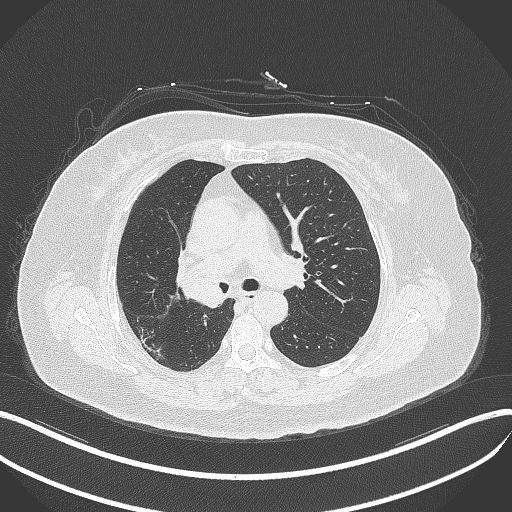
Chest CT, one axial slice; position 225 of 376 along the scan axis; reconstruction kernel B70f; 120 kVp; lung window (W 1500 / L -600 HU); 512 × 512 image matrix, field of view 400 × 400 mm. Female patient, age 60 years. Case-level facts recorded for this patient, not image findings: clinical TNM (as recorded): T1c N0 M0.
Annotated regions visible in this slice (bounding box drawn by a radiologist):
- lung tumour (recorded histology: squamous cell carcinoma): bounding box (x1, y1, x2, y2) in pixels: (174, 261, 232, 314)